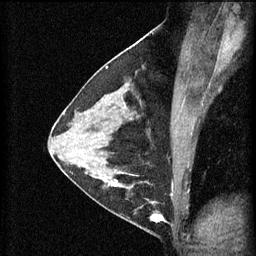
Breast MRI (dynamic contrast-enhanced), one sagittal slice; slice 32 of 60 in the series (ordered by position); 3 images stored at this slice position (order not interpretable as contrast timing); 1.5 T; TE 4.2 ms, TR 11 ms; 2 mm slice thickness; 256 × 256 image matrix, field of view 180 × 180 mm. Female patient, age 29 years.
Outlined on this slice (semi-automatic segmentation, software-assisted and operator-edited):
- analysis volume of interest (the breast-tissue region the enhancement analysis was run in; not a lesion): box from (x=105, y=172) to (x=169, y=227) px
- tumour enhancement mask (voxels above the 70 % enhancement threshold inside the analysis volume of interest): (x=109, y=172)–(x=169, y=223)